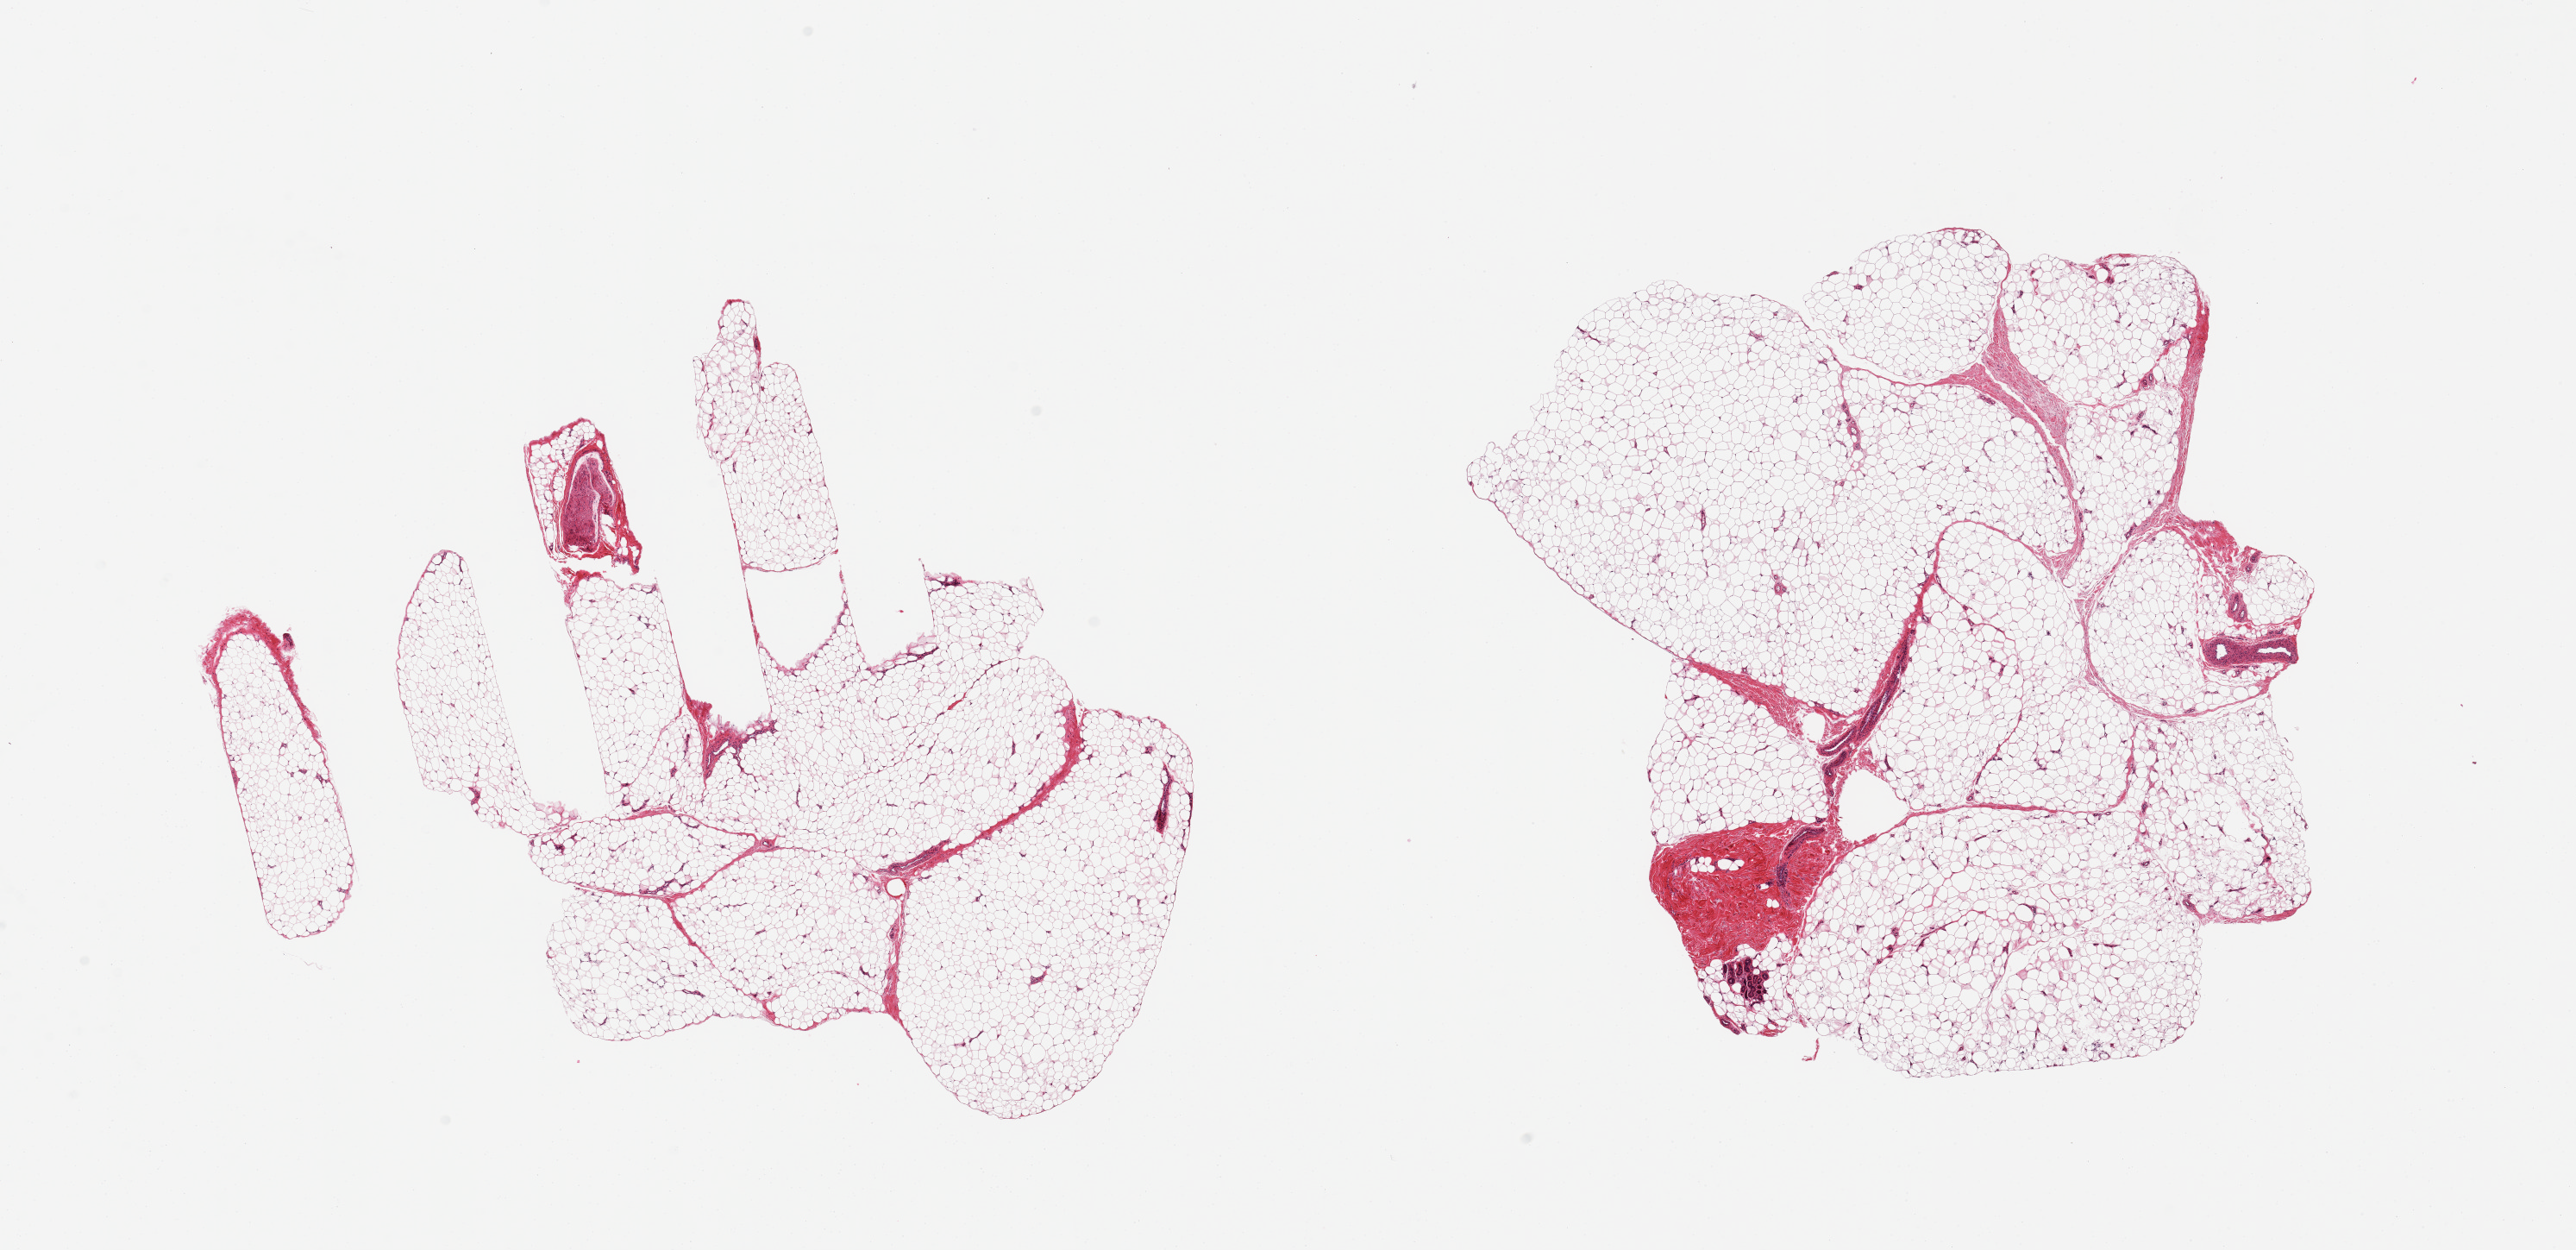
Digitized hematoxylin and eosin (H&E)-stained section, low-resolution overview of the scanned area, about 23.6 x 11.5 mm (slide scanned at 20x), PAXgene-fixed, paraffin-embedded tissue, target tissue: adipose tissue, donor tissue sample. Donor: male.
Review note (as recorded): 2 pieces; 10 & 5% fibroneurovascular content; small (0.5mm) focus of sweat glands.